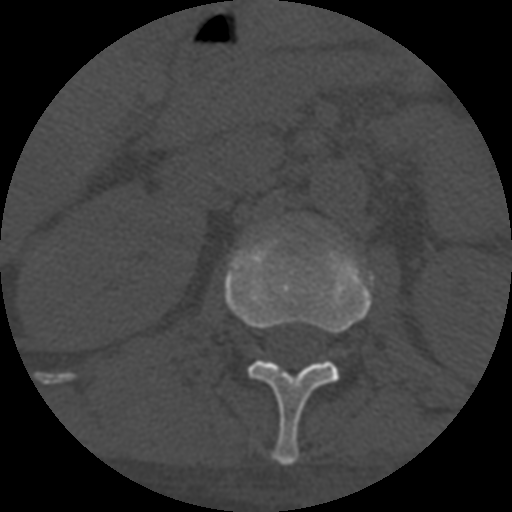
CT including the spine, one axial slice; position 280 of 708 along the scan axis; reconstruction kernel STANDARD; 120 kVp; one of 3 acquisitions stored at this slice position; bone window (W 1800 / L 400 HU); 1.25 mm slice thickness; 512 × 512 image matrix. Patient age 55 years. From the clinical record (not read from this slice): primary cancer: colon; vertebrae with lytic lesions (as recorded): T12, L1, L5.
Outlined on this slice (semi-automatically segmented with operator editing):
- L1 vertebra: box from (x=224, y=227) to (x=374, y=466) px